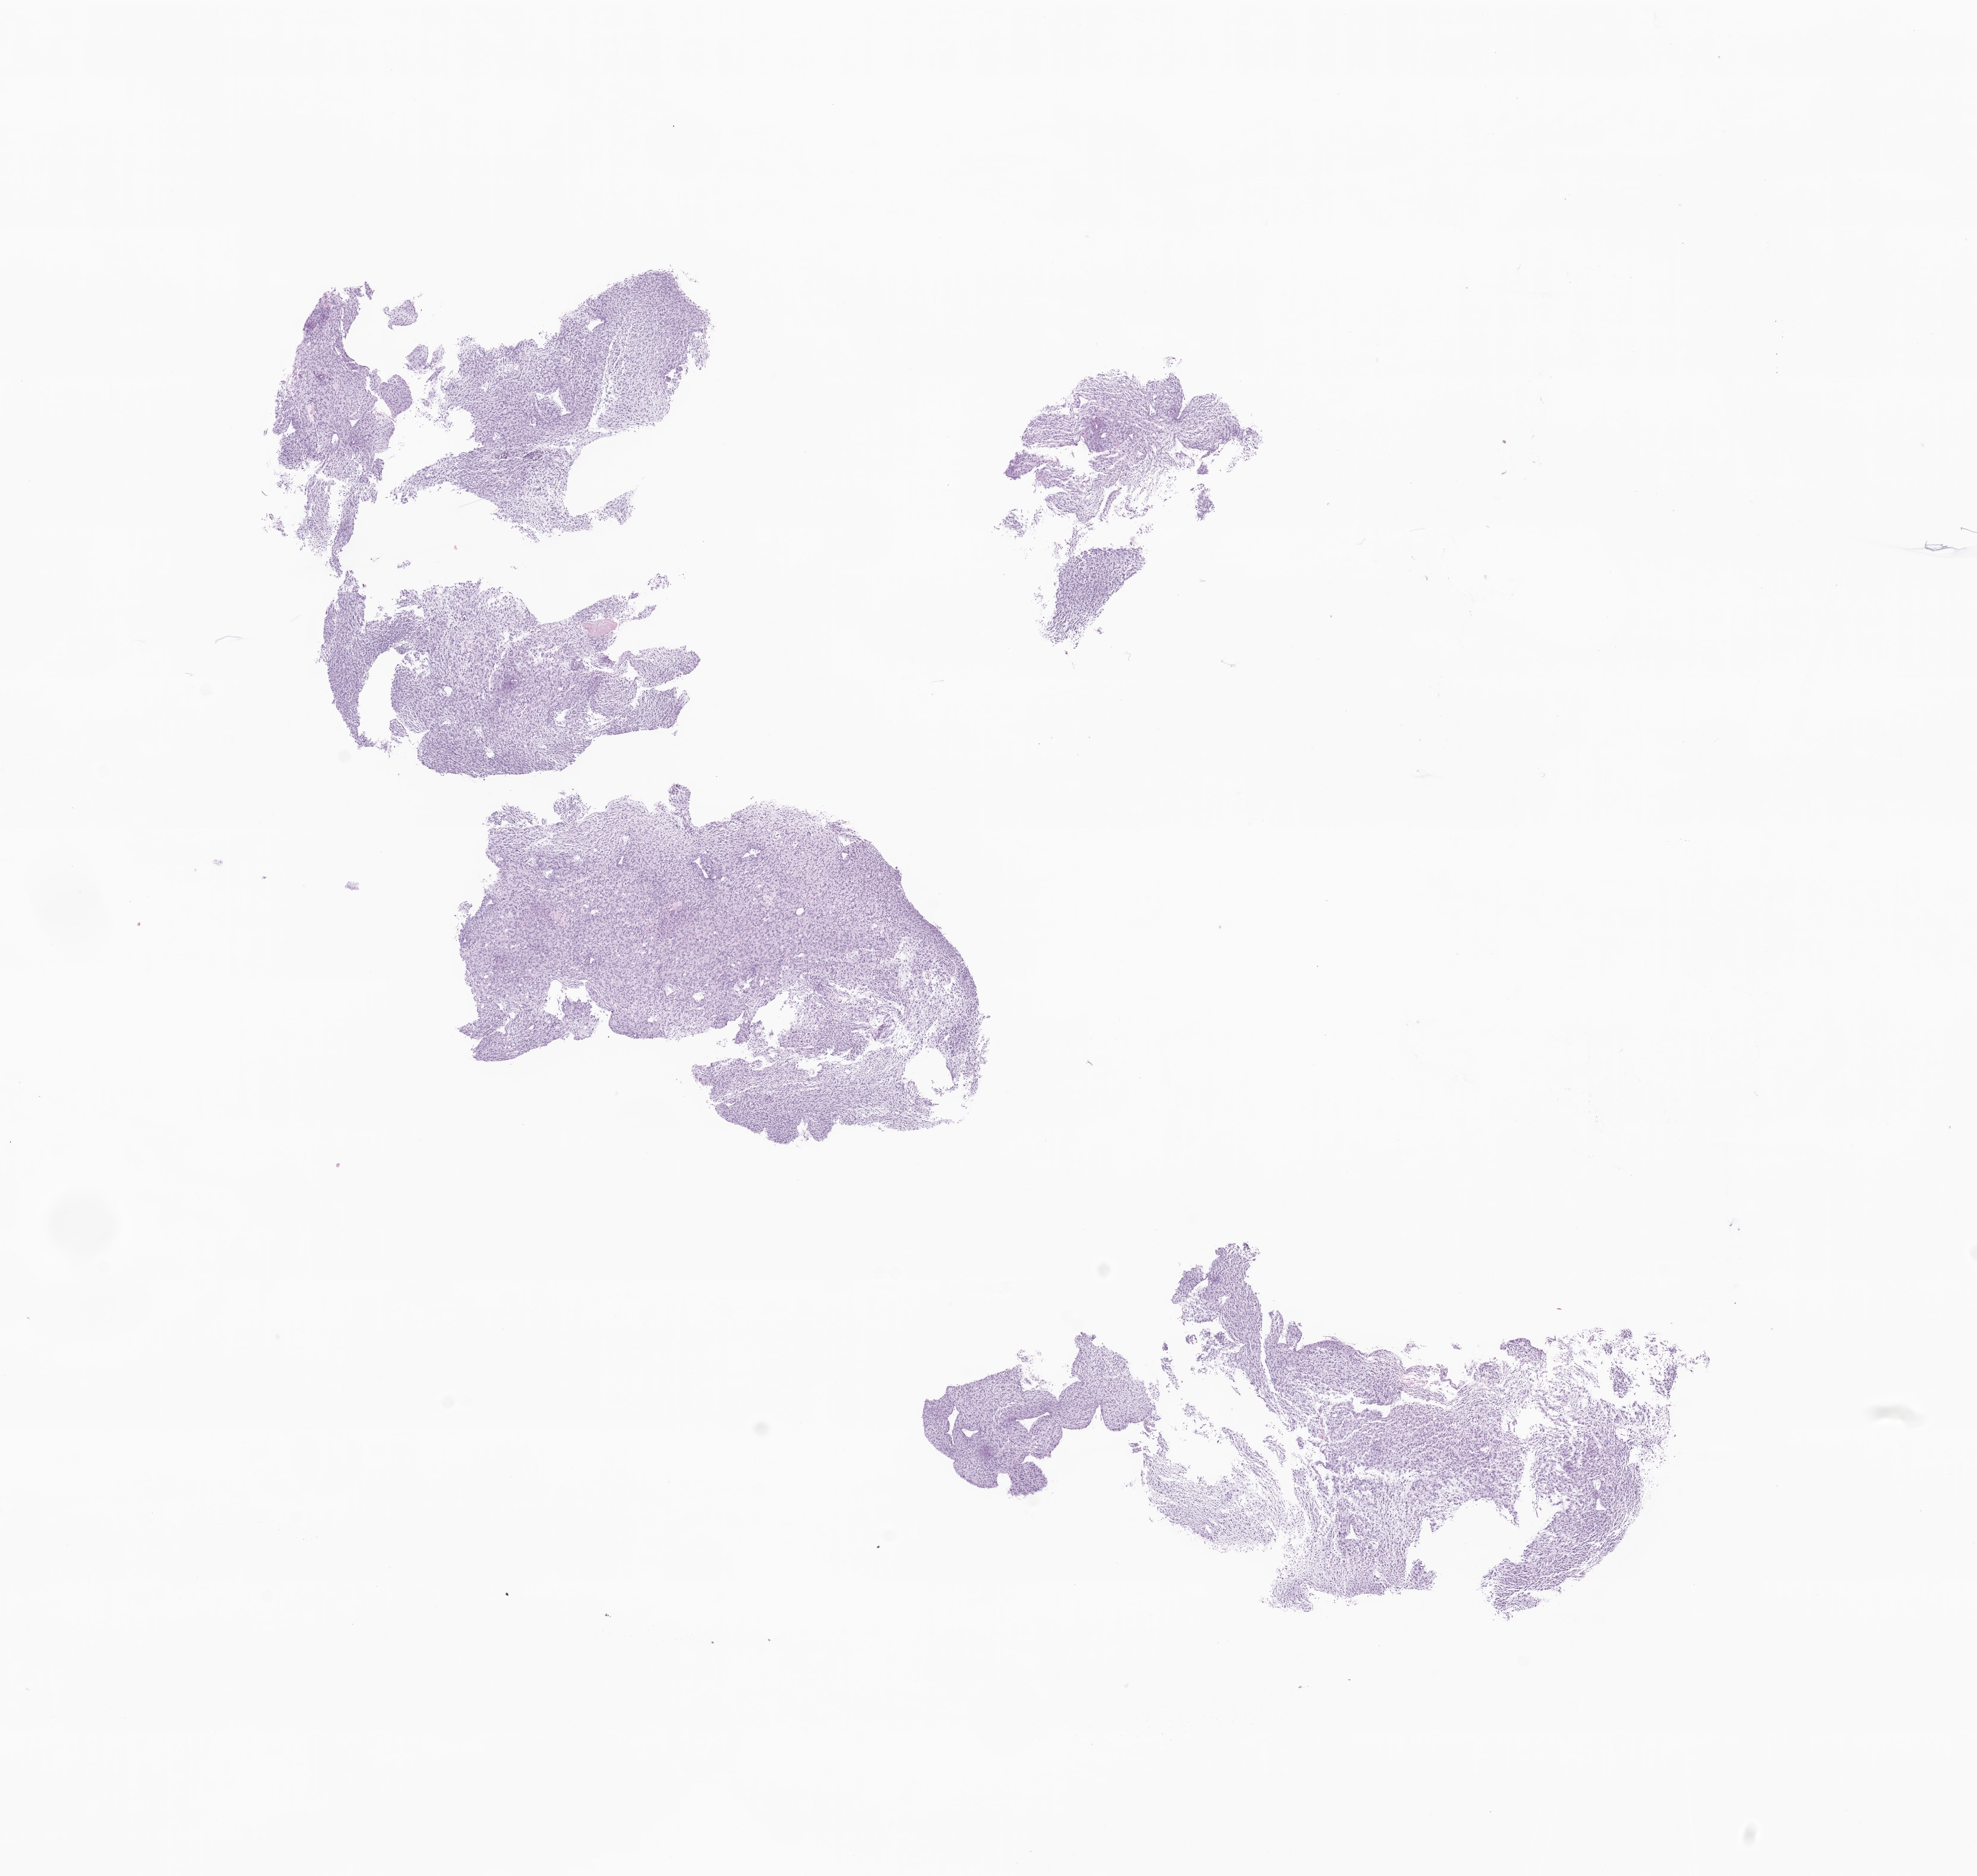
Digitized hematoxylin and eosin (H&E)-stained section of tumor tissue from the brain — a low-resolution overview of the entire scanned area, about 14.0 x 13.3 mm, formalin-fixed paraffin-embedded section. Female patient, age 108 months (9 years).
Diagnosis: Glioma, malignant.